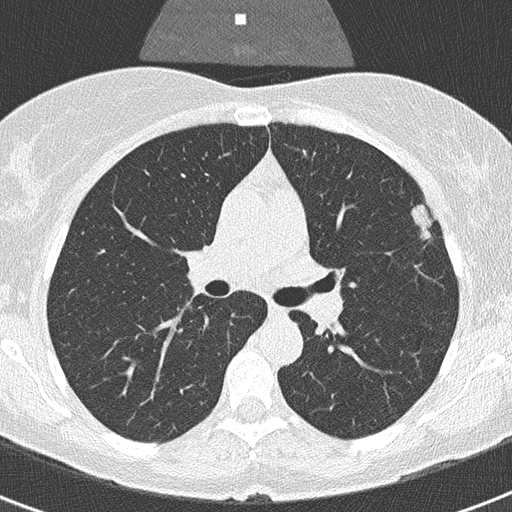
Low-dose screening chest CT, one axial slice. Position 205 of 320 along the scan axis. 120 kVp. Lung window (W 1500 / L -600 HU). 2 mm slice thickness. 512 × 512 image matrix.
Annotated regions visible in this slice (expert manual segmentation):
- lesion 1 (tumor, upper lobe of left lung): bounding box [x1, y1, x2, y2] px = [410, 205, 432, 239]